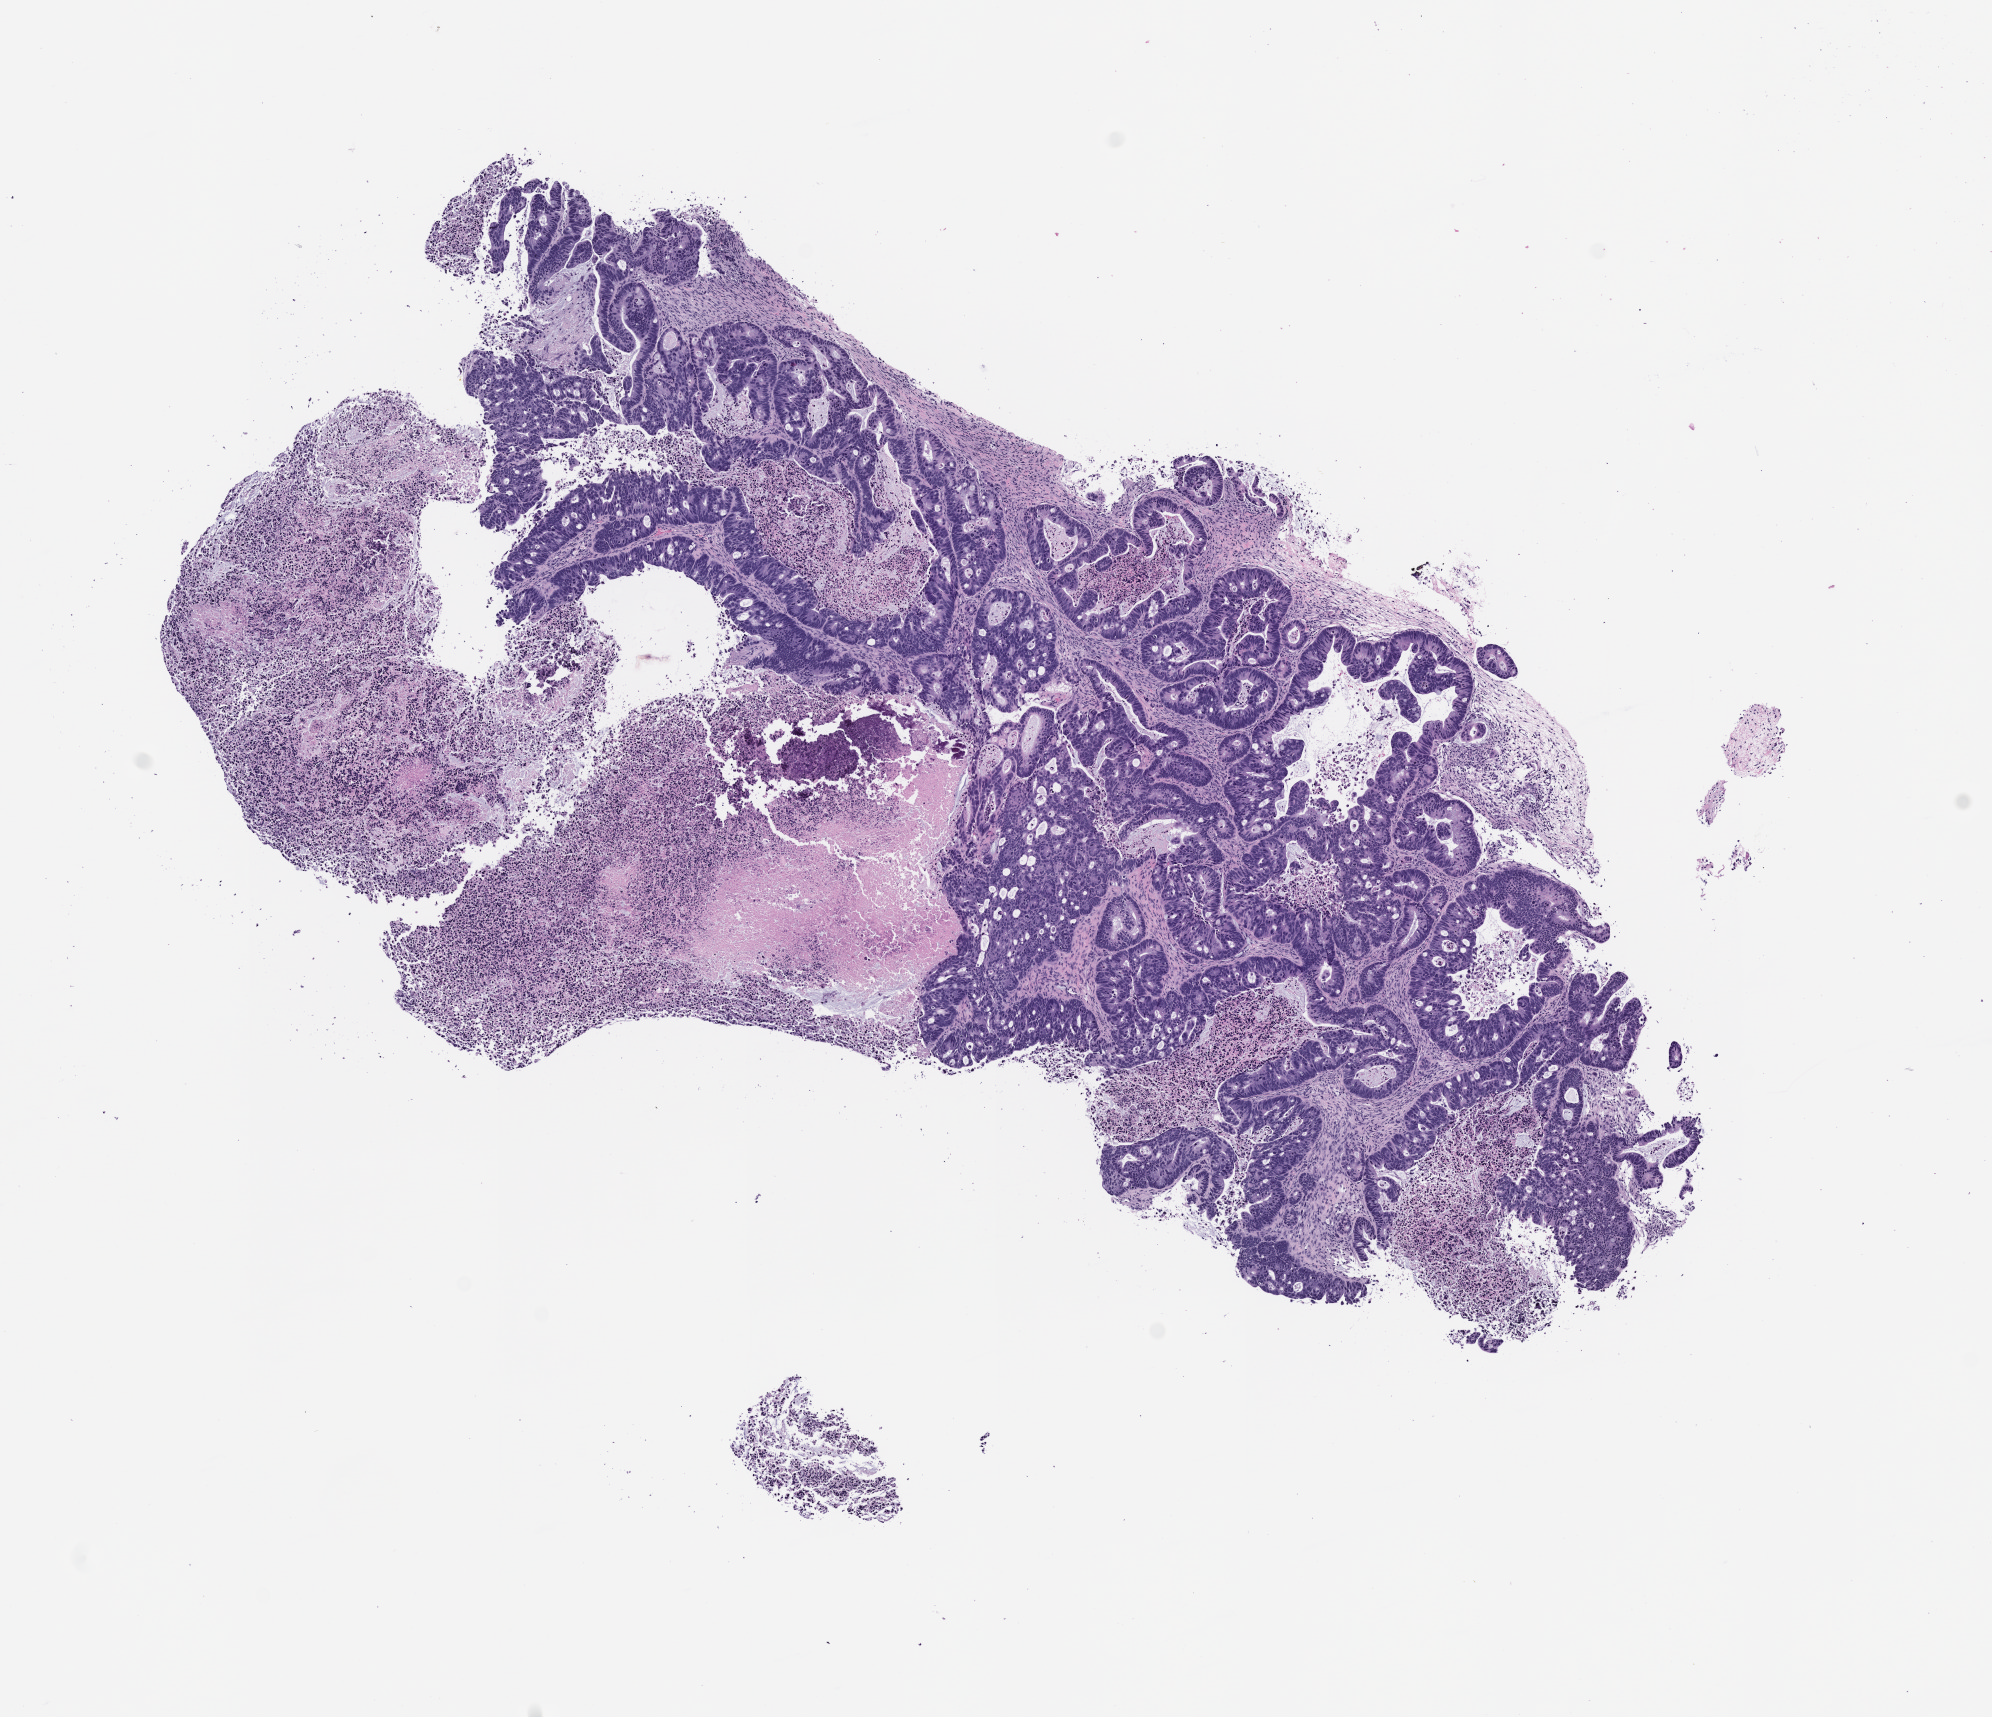
Hematoxylin and eosin (H&E) whole-slide image of a patient-derived xenograft (PDX) tumor grown in a mouse, passage 1 — shown as a low-resolution overview of the whole scanned area (about 8.0 x 6.9 mm). FFPE section. Originating tumor site category: gastrointestinal tract.
- originating patient diagnosis: Colorectal Carcinoma